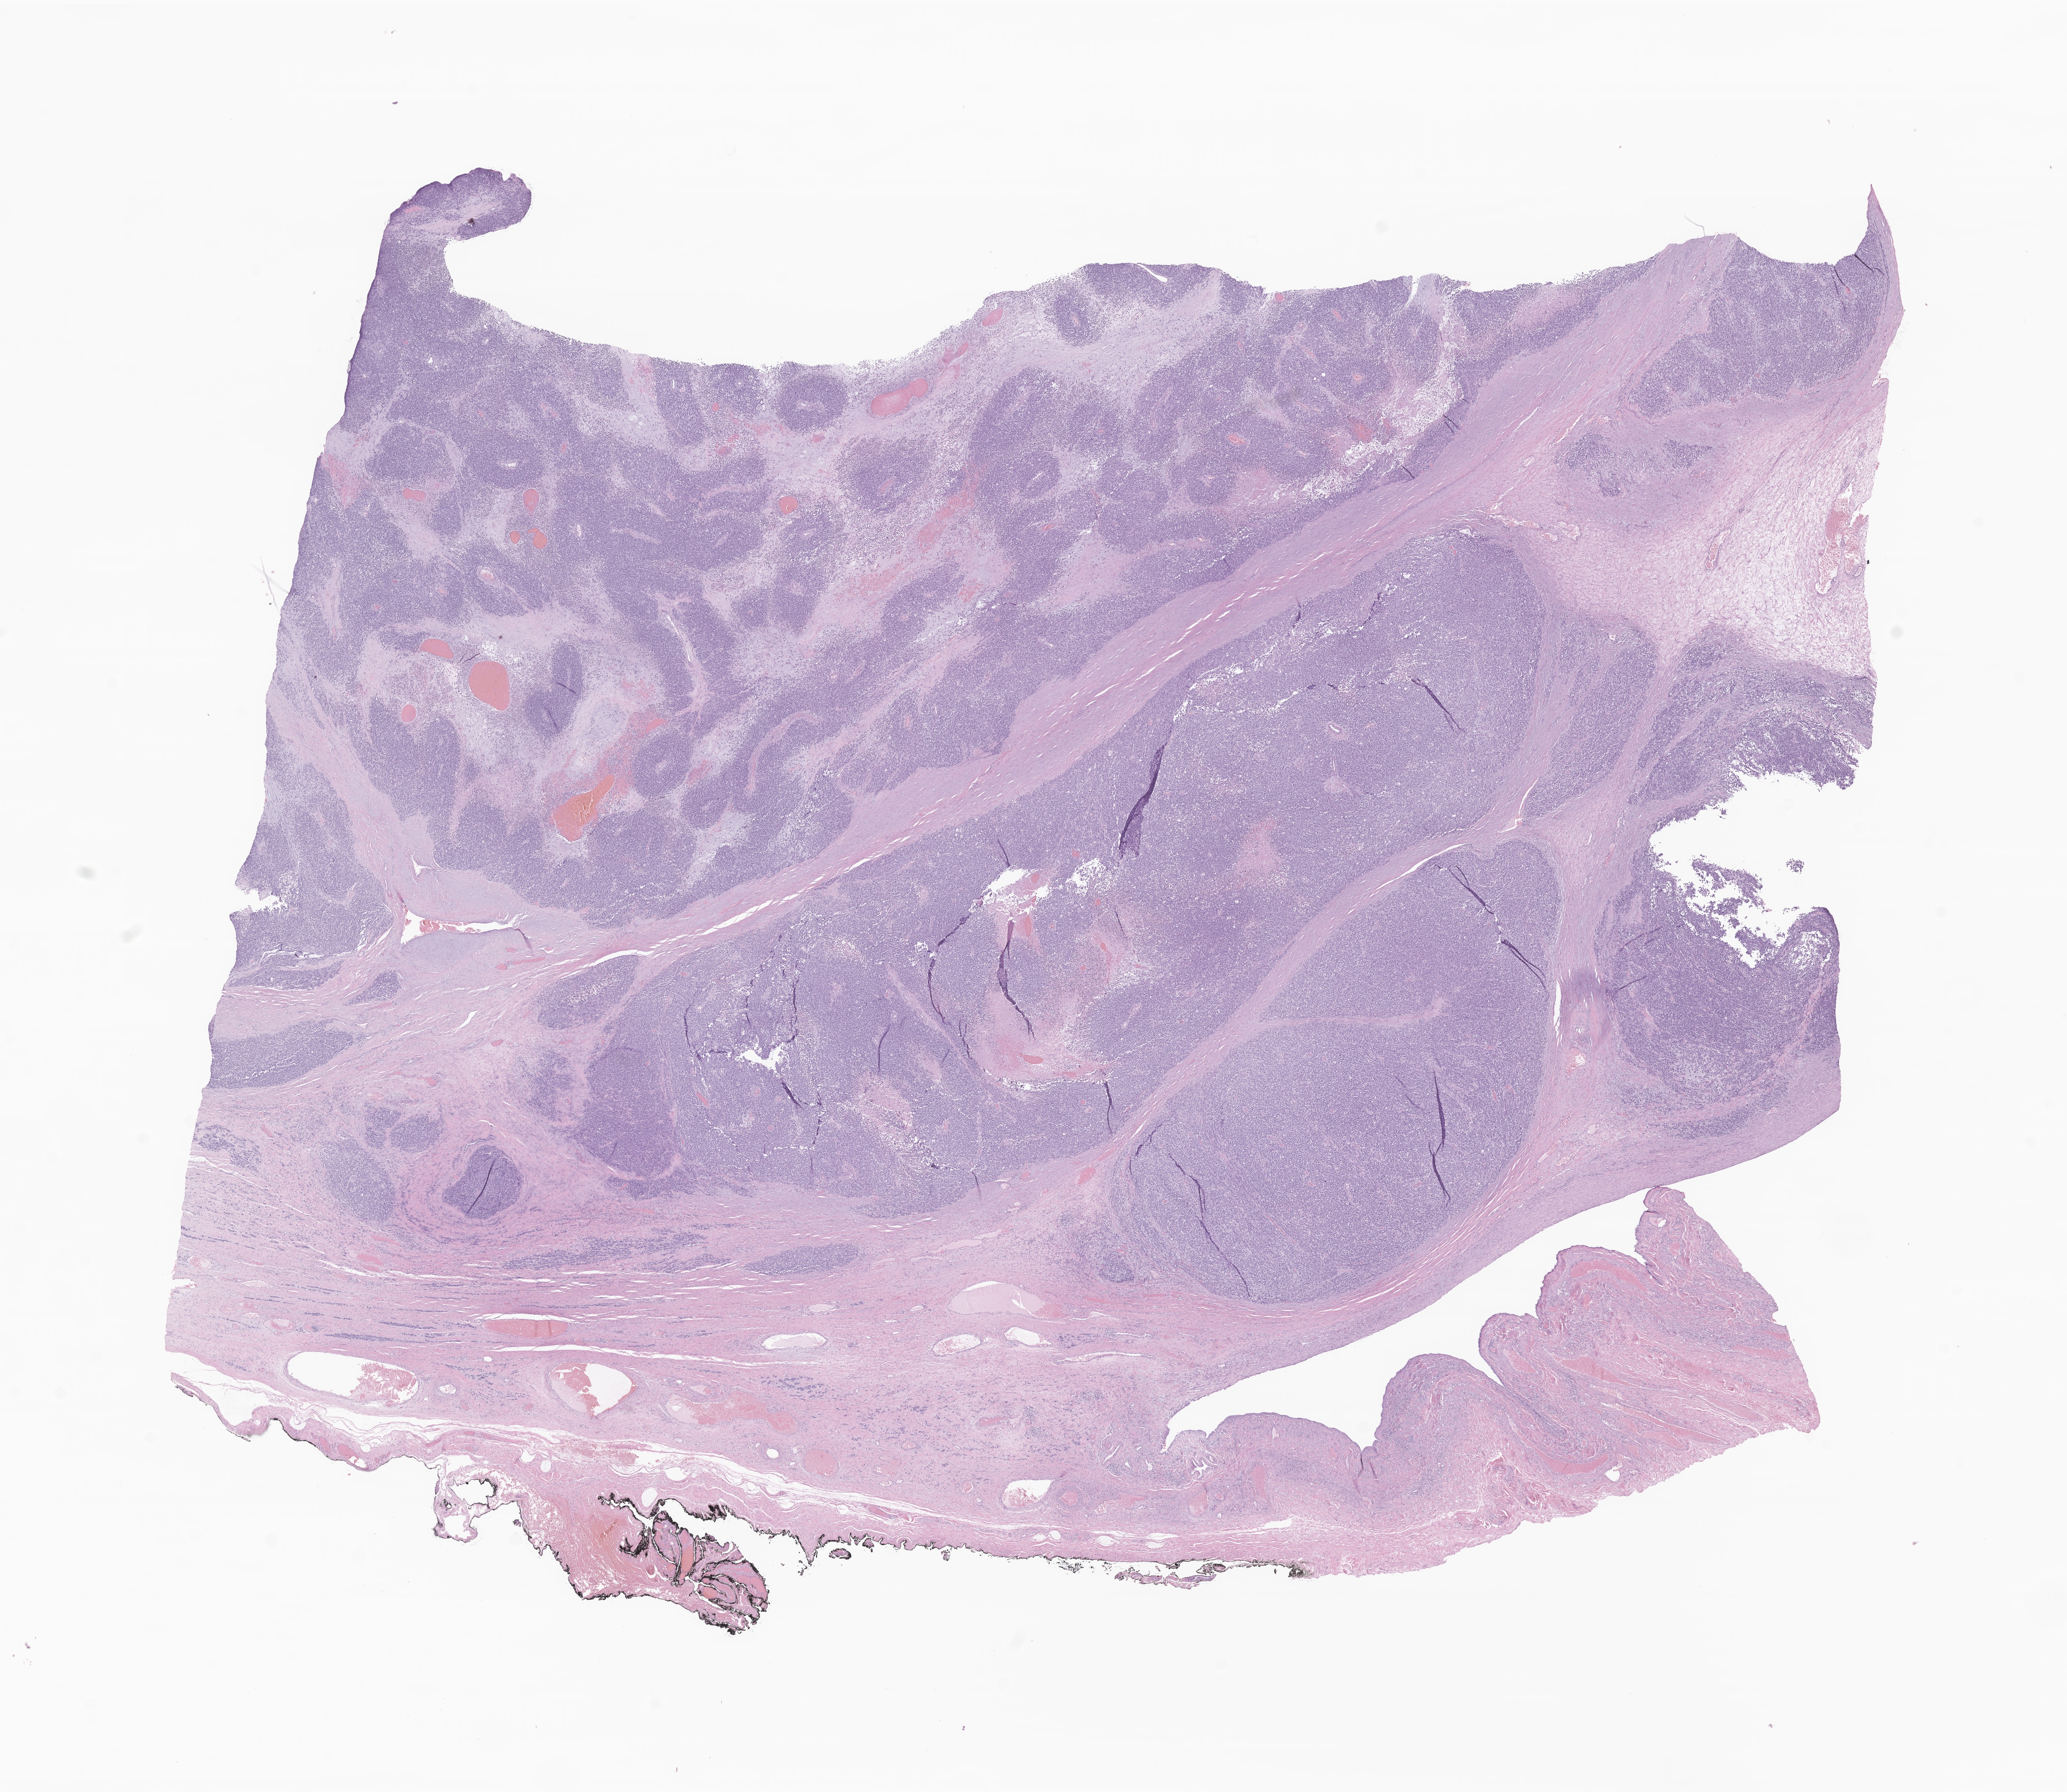
Digitized hematoxylin and eosin (H&E)-stained section of tumor tissue from the testis — a low-resolution overview of the entire scanned area, about 23.4 x 20.3 mm; formalin-fixed paraffin-embedded section. Patient: male, age 197 months (16 years 5 months).
Recorded diagnosis: Embryonal rhabdomyosarcoma, NOS.